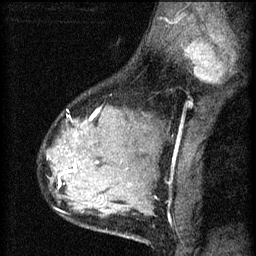
Breast MRI (dynamic contrast-enhanced), one sagittal slice. Position 45 of 60 along the scan axis. 3 images stored at this slice position (order not interpretable as contrast timing). 1.5 T. TE 4.2 ms, TR 8.2 ms. 256 × 256 image matrix, field of view 180 × 180 mm. Female patient, age 37 years.
Structures marked on this image (semi-automatically segmented with operator editing):
- analysis volume of interest (the breast-tissue region the enhancement analysis was run in; not a lesion): bounding box [x1, y1, x2, y2] px = [49, 110, 119, 197]
- tumour enhancement mask (voxels above the 70 % enhancement threshold inside the analysis volume of interest): [61, 164, 78, 187]